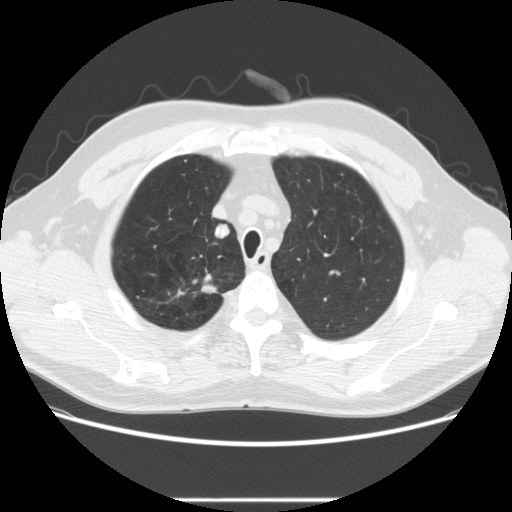
Chest CT (low-dose screening protocol), one axial image. First (baseline) screen. Lung window (W 1500 / L -600 HU). Male participant, aged 64 years at enrolment. Former smoker at enrolment.
2 lesions marked by an expert reader on this slice (largest first), bounding box <169,275,226,306> (left, top, right, bottom; pixels); <205,220,237,247>. The screening reader recorded 2 non-calcified nodules or masses ≥4 mm on this exam; which of them these boxes mark is not recorded. Official screen result: positive, change unspecified: nodule(s) >= 4 mm or enlarging nodule(s), mass(es), or other non-specific abnormalities suspicious for lung cancer. Lung cancer was diagnosed 753 days after this screen (after the third annual screen): adenocarcinoma, NOS, right upper lobe, moderately differentiated (G2), stage IA (AJCC 6th edition), 14 mm at pathology.